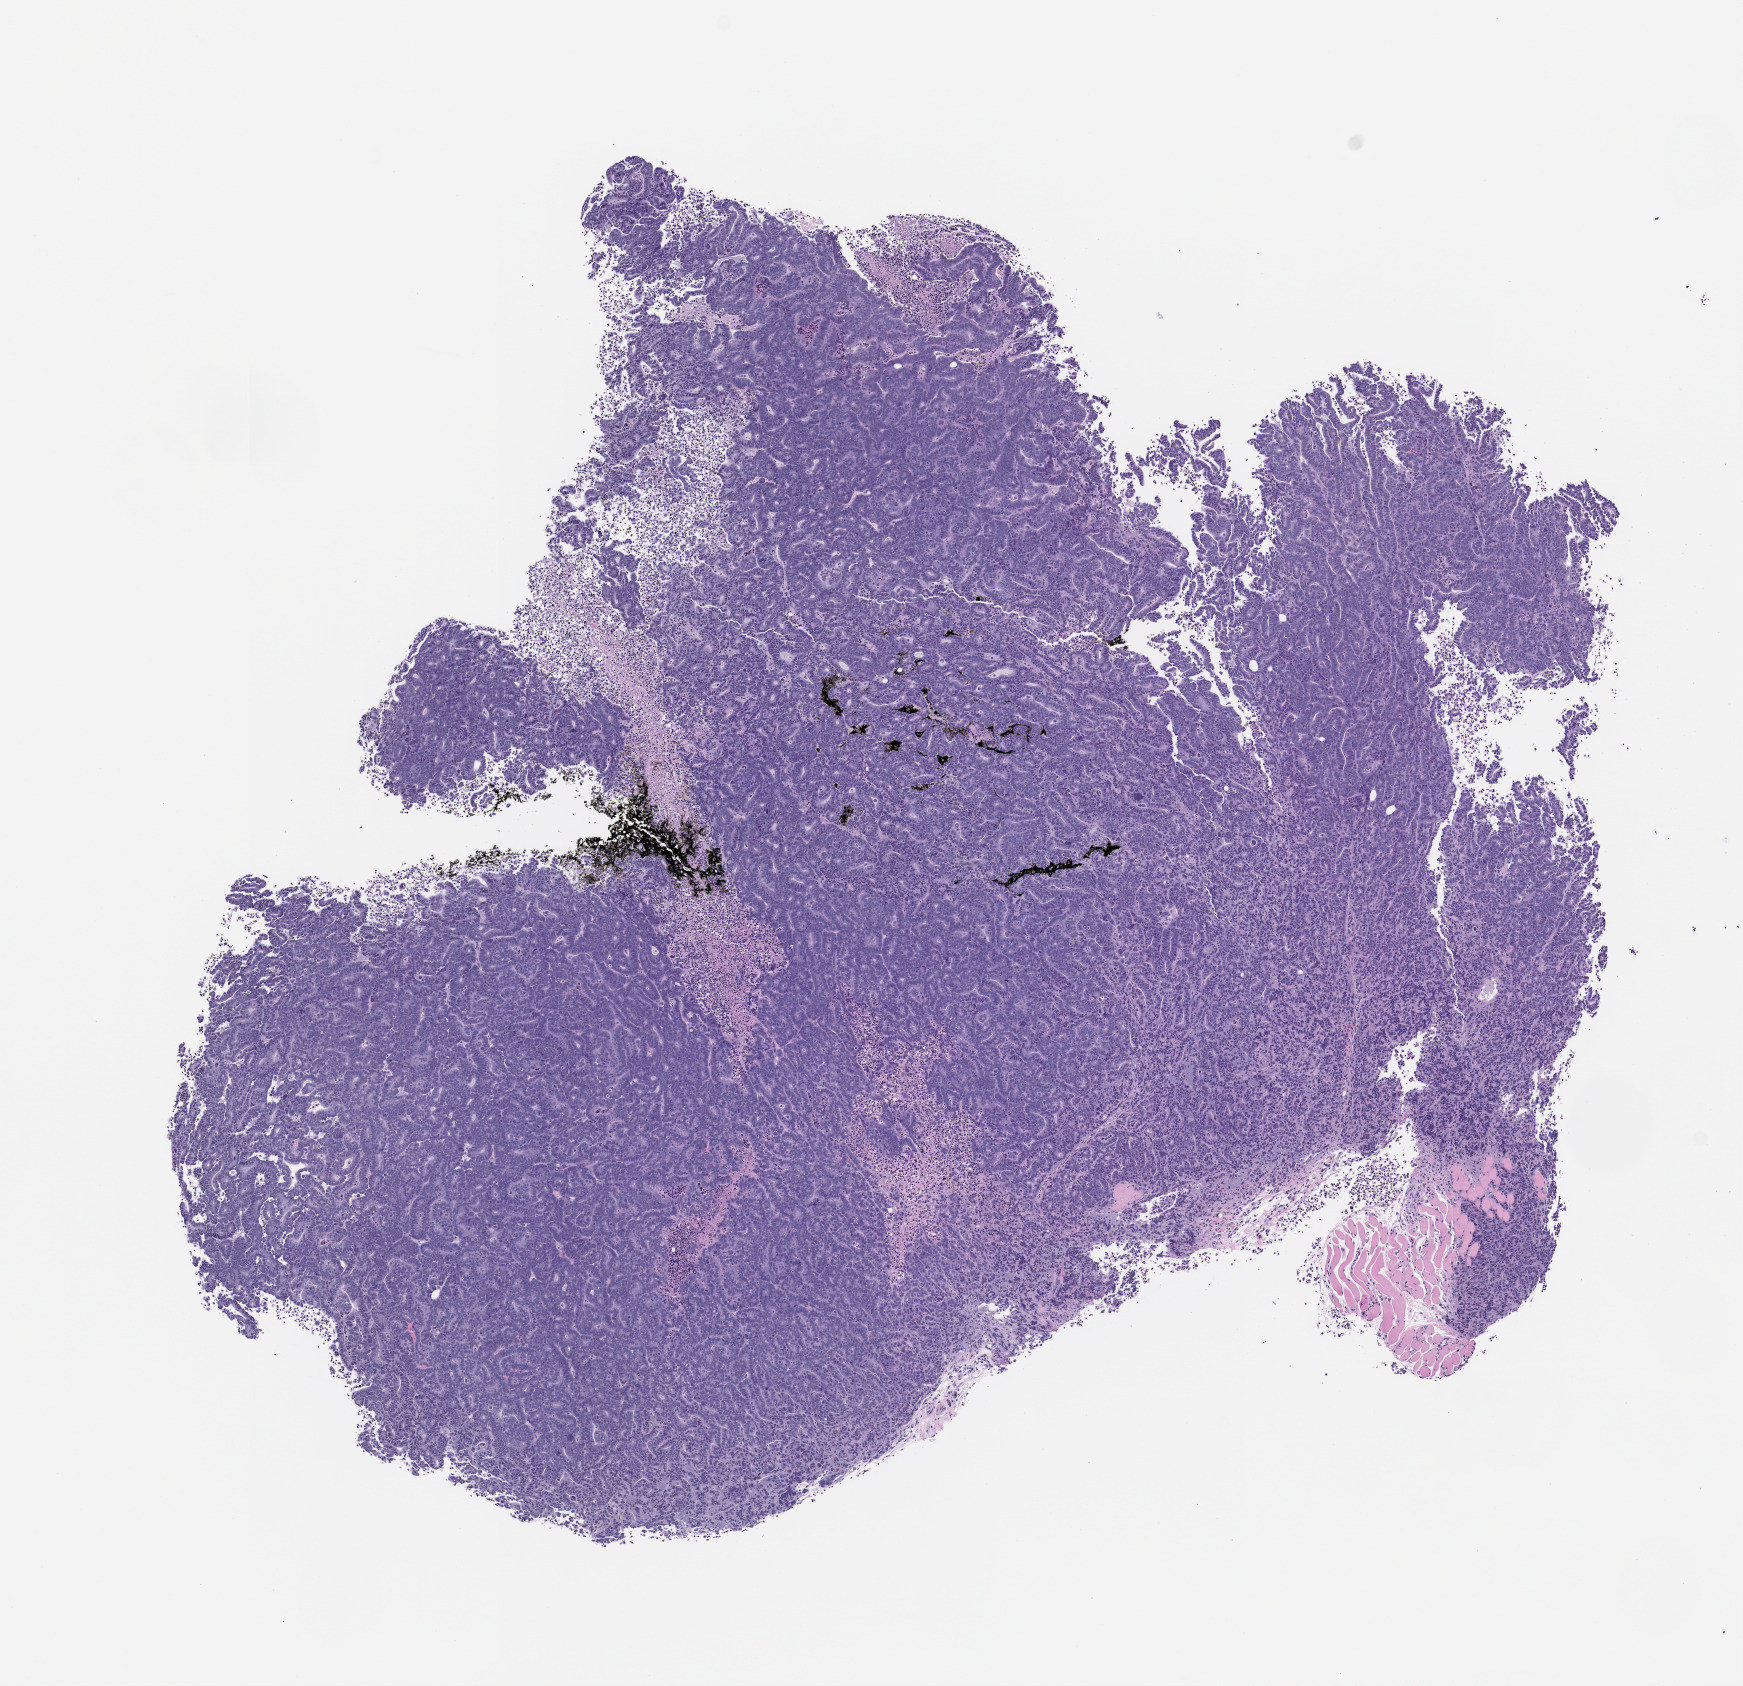
Whole-slide image, hematoxylin and eosin (H&E): patient-derived xenograft (human tumor grown in a mouse) — whole scanned area (about 7.0 x 6.8 mm) shown as a low-resolution overview, FFPE section, originating tumor site category: small intestine.
• originating patient diagnosis: Small Intestinal Adenocarcinoma